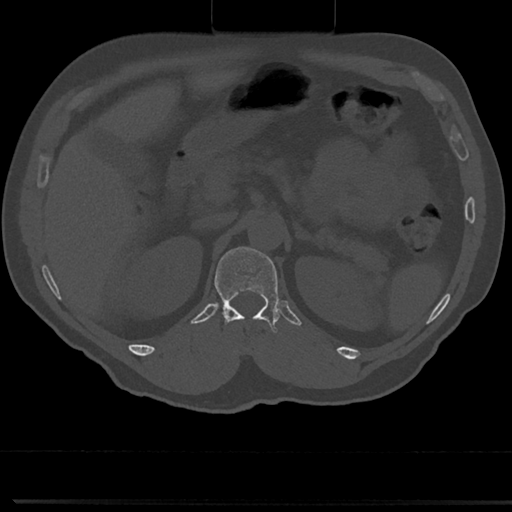
CT including the spine, one axial slice. Position 143 of 817 along the scan axis. Reconstruction kernel Br40s/3. 120 kVp. Bone window (W 1800 / L 400 HU). 0.5 mm slice thickness. 512 × 512 image matrix, field of view 355 × 355 mm. Patient: male, 61 years. From the clinical record (not read from this slice): primary cancer: prostate.
Annotated regions visible in this slice (semi-automatic segmentation, software-assisted and operator-edited):
- T12 vertebra: bounding box <211,247,281,354> (left, top, right, bottom; pixels)